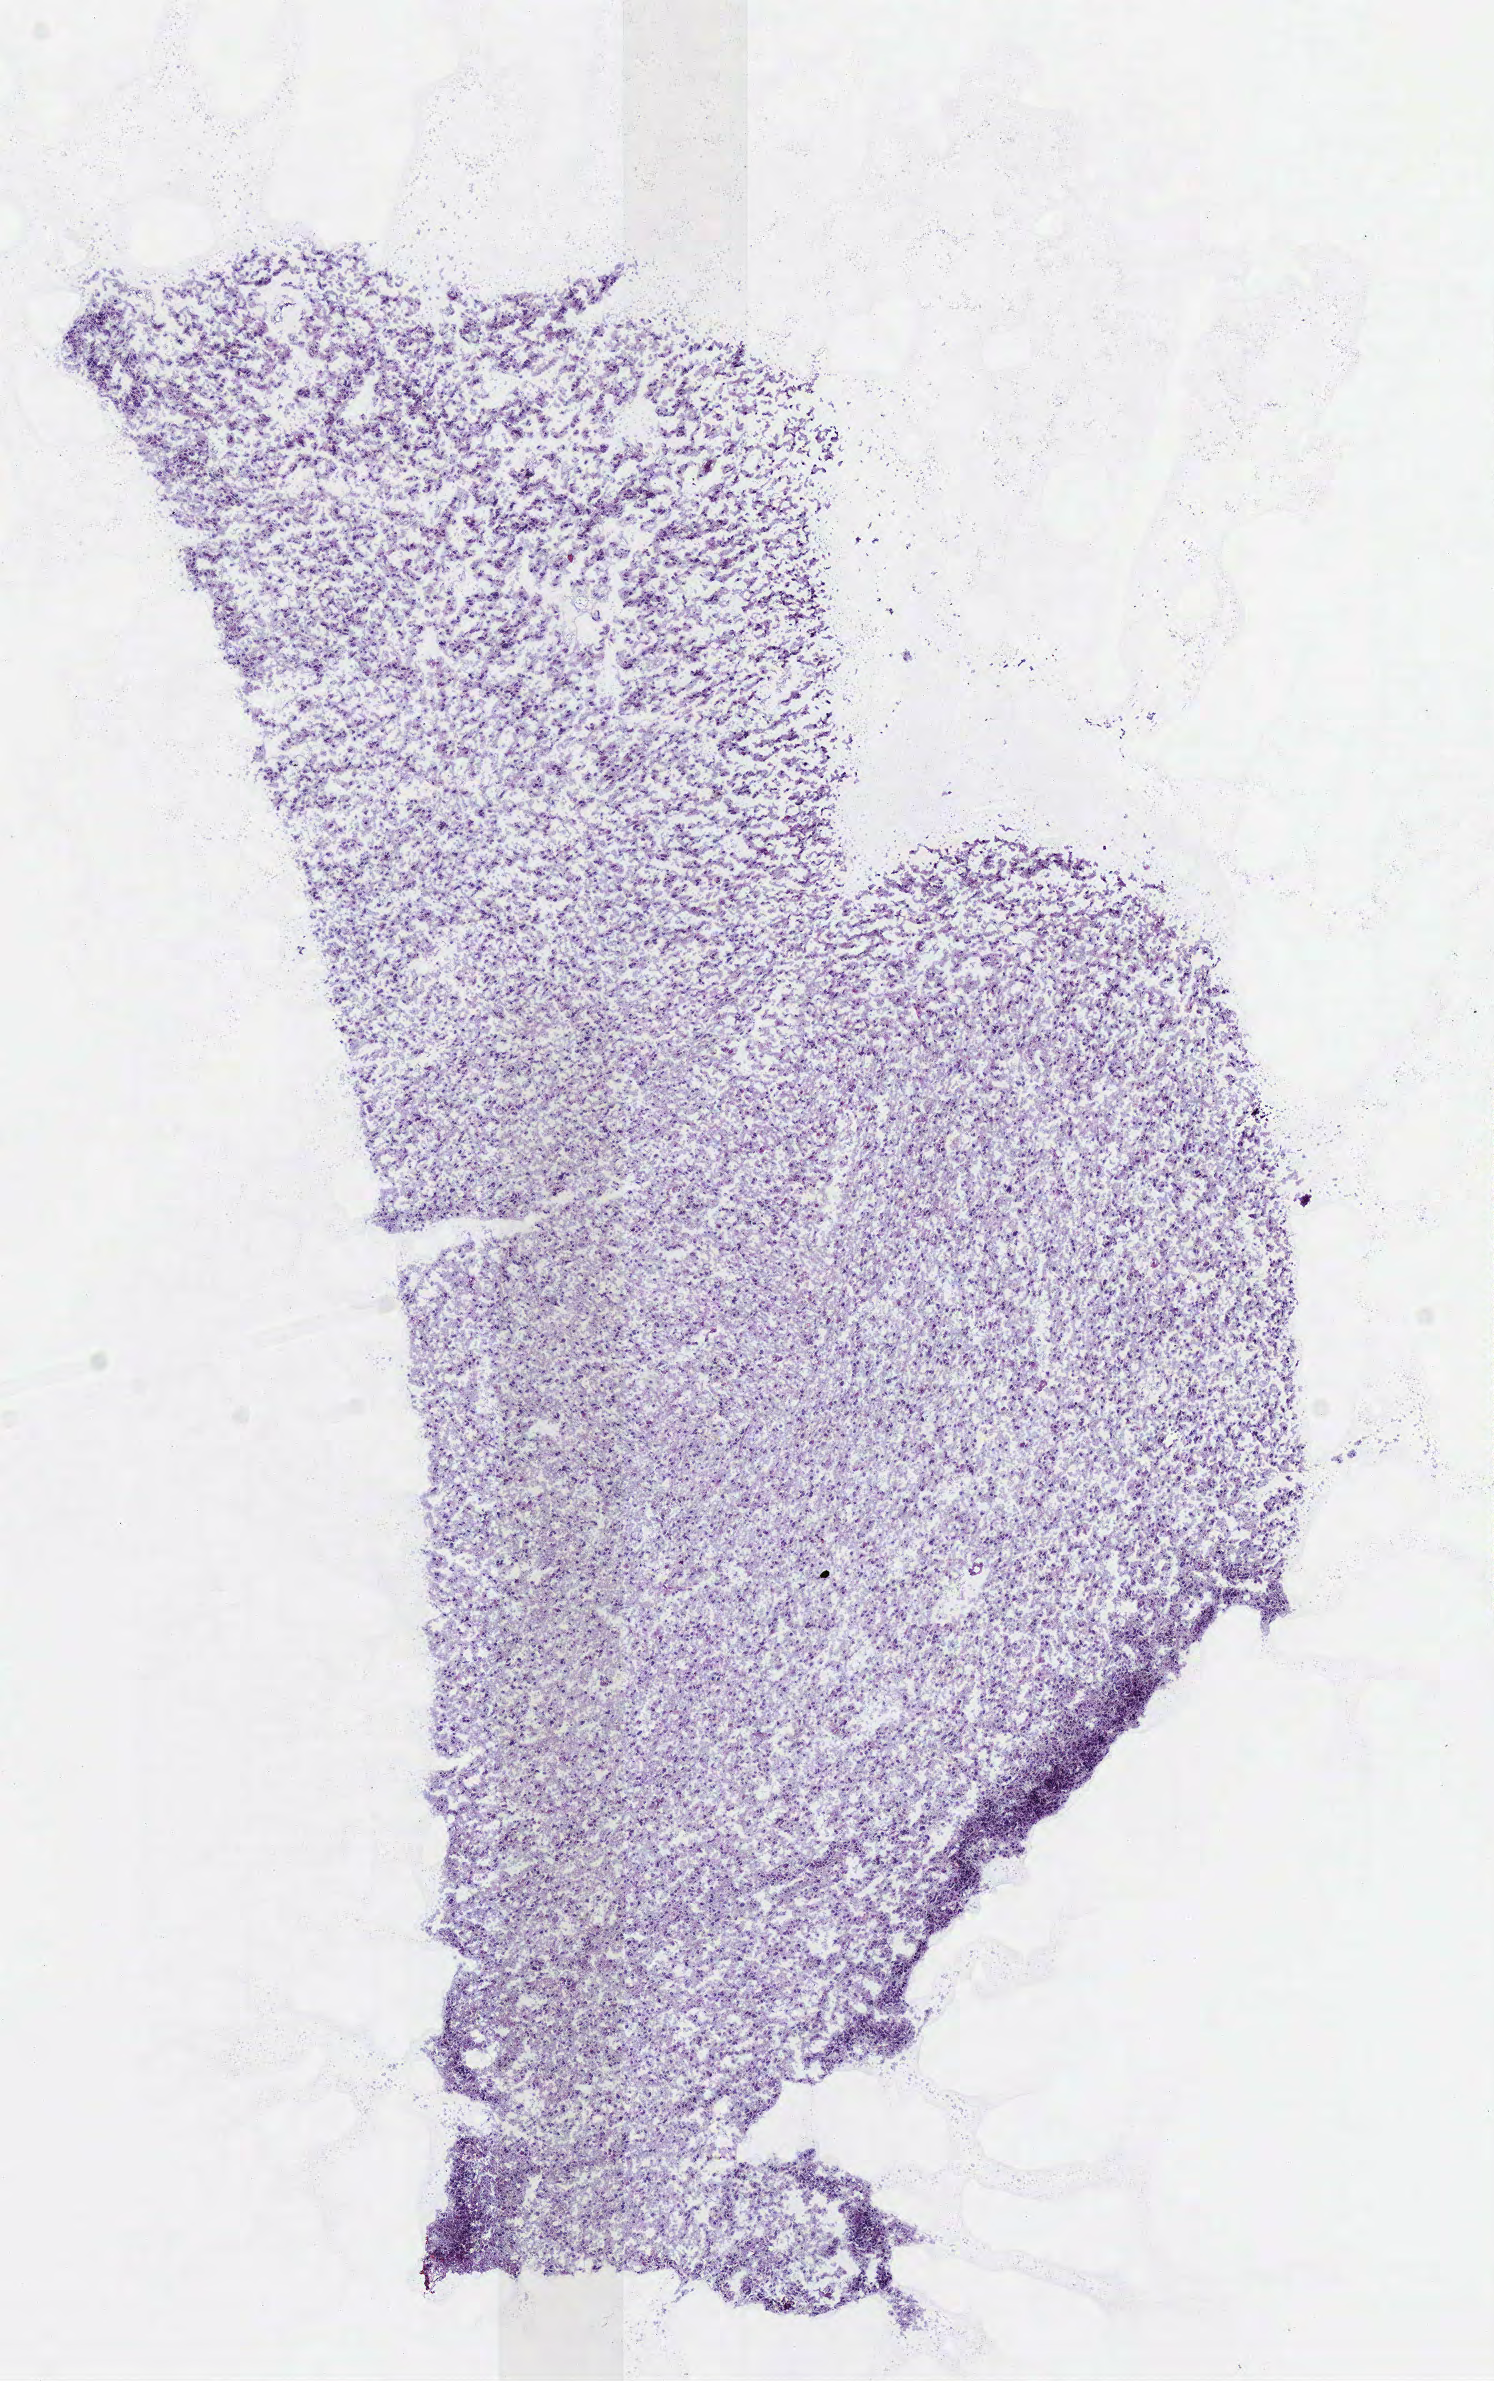
Whole-slide histology image, H&E-stained — shown as a low-resolution overview of the whole scanned area (about 5.9 x 9.4 mm, from a 40x scan), frozen section from the bottom of the tissue portion, brain, primary tumour sample. Patient: female, age at initial diagnosis 41 years. Histologic grade: G2 (moderately differentiated). Composition of this section per pathologist review: tumour cells 100%, tumour nuclei 75%, normal cells 0%, stromal cells 0%, necrosis 0%.
Pathologic diagnosis: Oligodendroglioma, NOS (cerebrum).